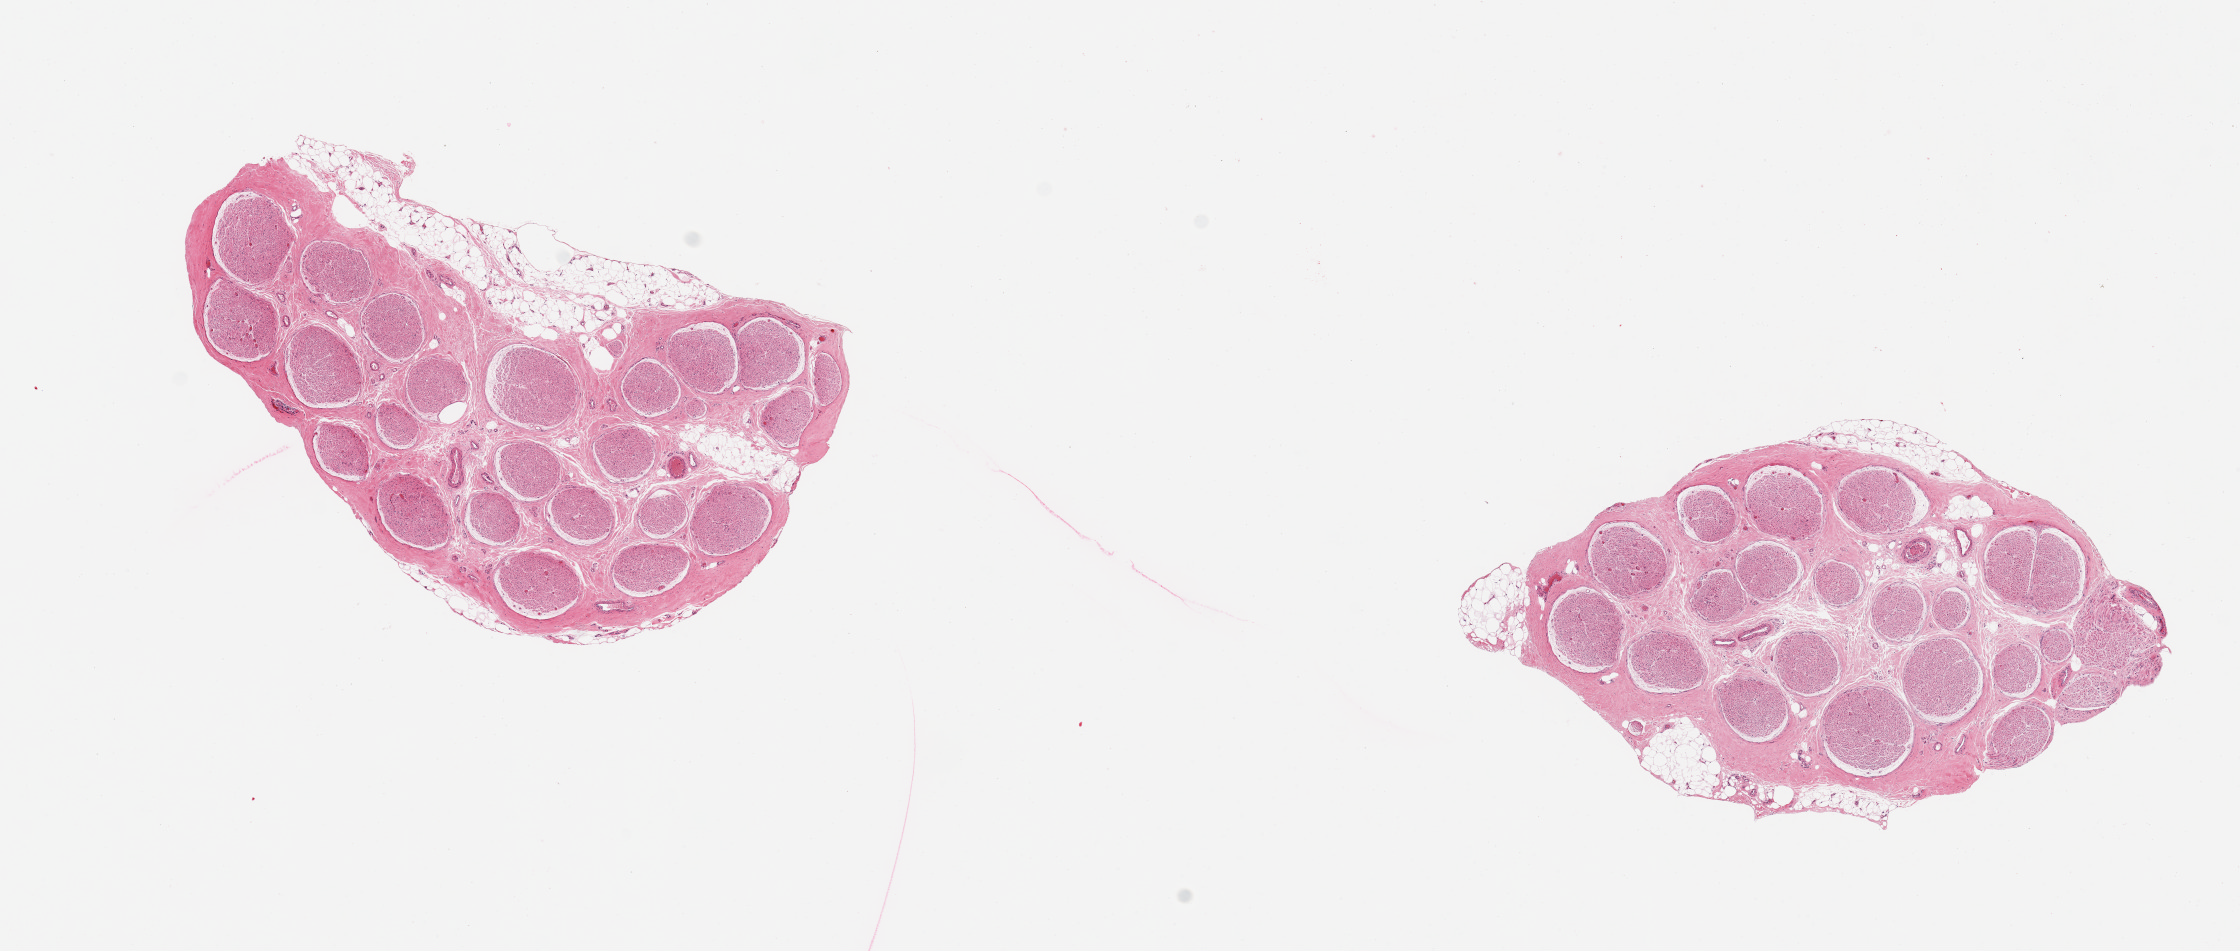
Haematoxylin and eosin whole-slide image, brightfield, whole scanned area (about 17.7 x 7.5 mm) shown as a low-resolution overview, PAXgene-fixed paraffin-embedded (PFPE) section, section of tibial nerve (target tissue), donor tissue sample.
Pathologist's review note for this sample: 2 pieces; ~0.75 and 0.5 mm attached external fat.